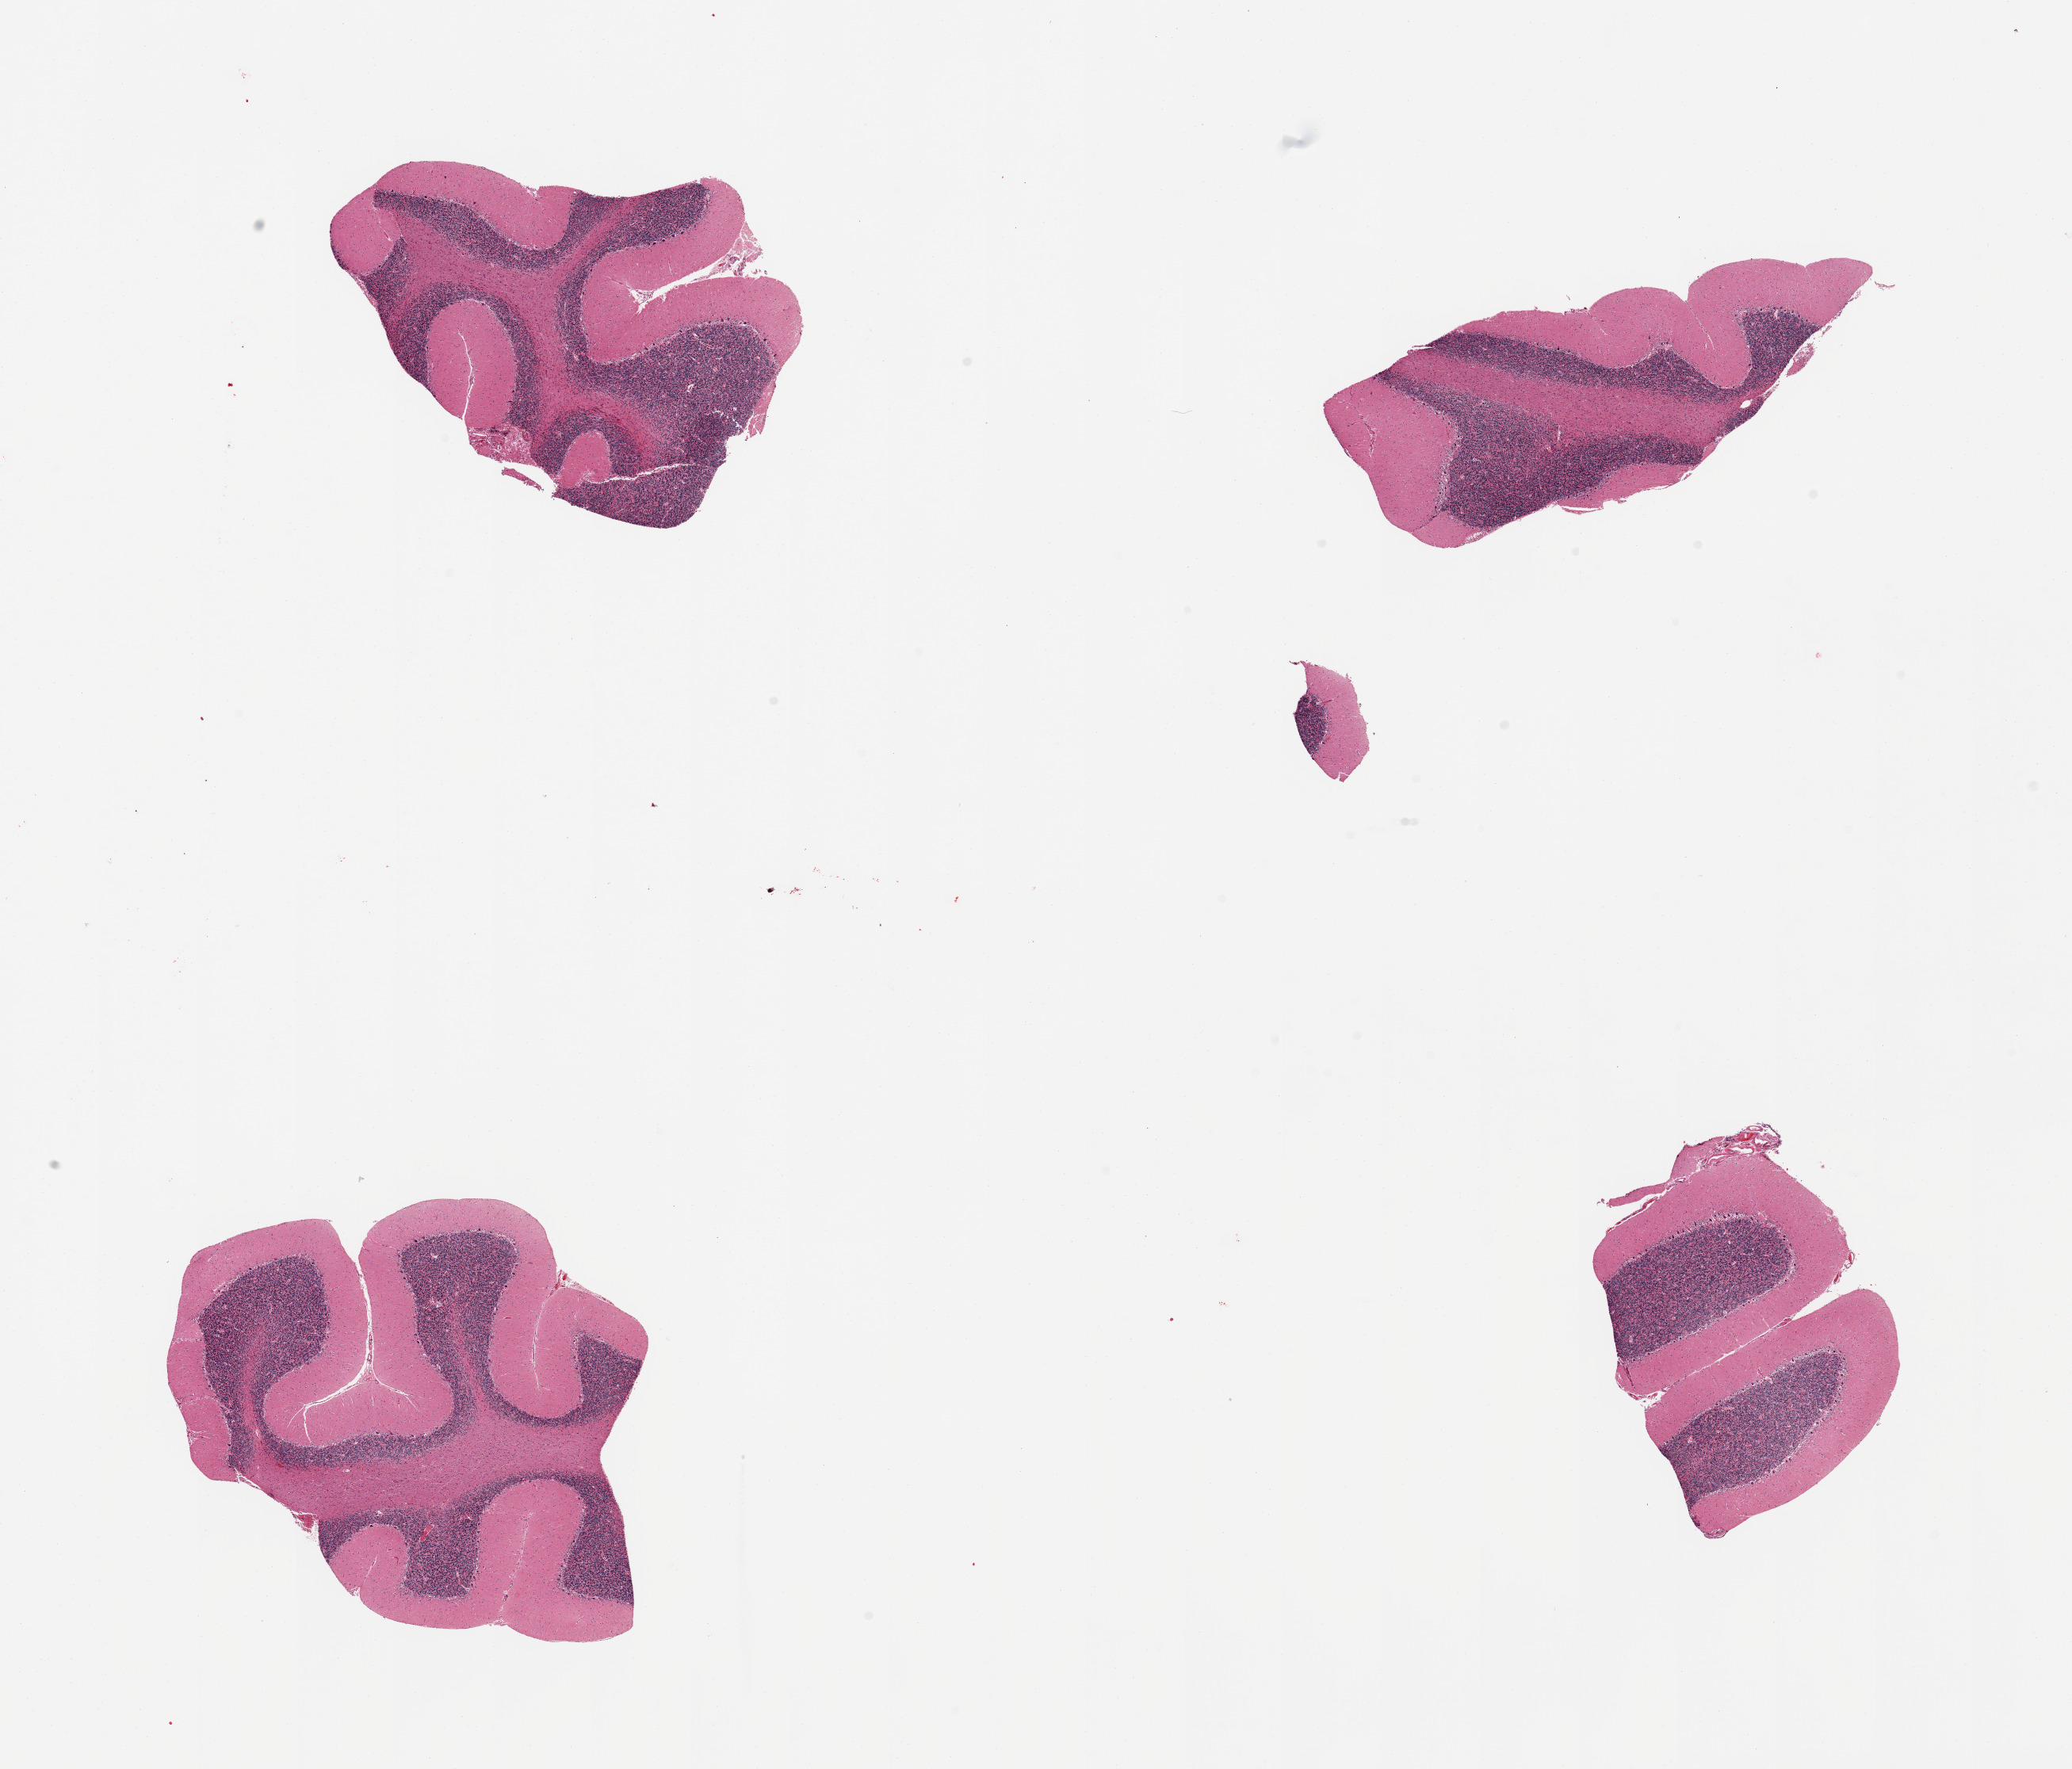
H&E whole-slide image — shown as a low-resolution overview of the whole scanned area (about 20.7 x 17.7 mm). PAXgene-fixed, paraffin-embedded tissue. Sampled site (target tissue): cerebellum. Tissue donor sample. Donor: male.
Reviewer comment on this tissue sample: 4 pieces.